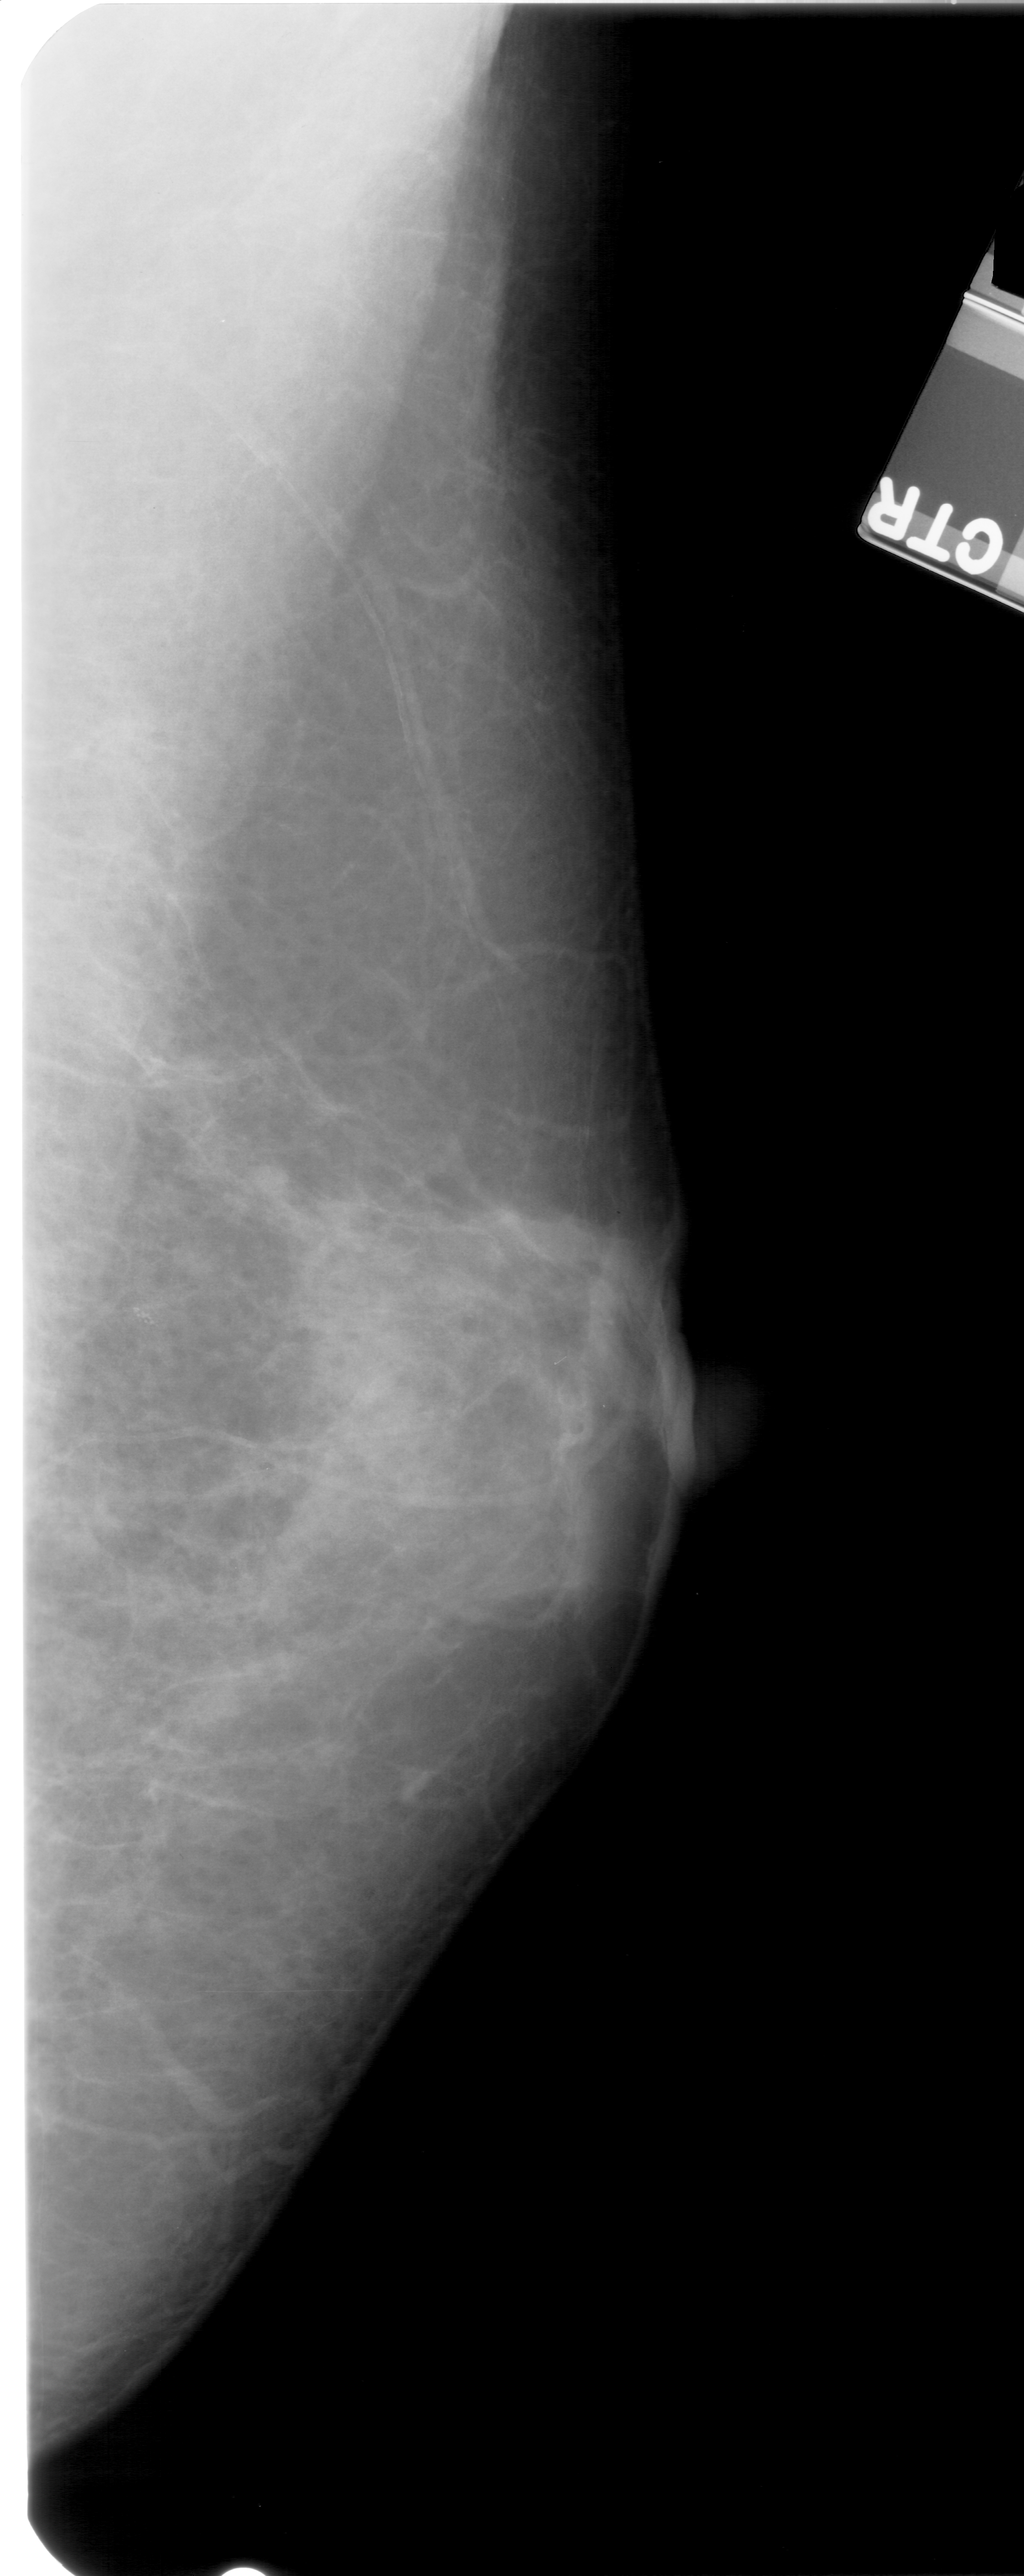
Mammogram (digitized film). Right breast. MLO view. Breast composition: extremely dense (BI-RADS density category 4 of 4). 1024 × 2576 image matrix.
Expert-marked regions of interest on this film, with their recorded descriptors:
- calcifications, morphology pleomorphic, distribution clustered; BI-RADS assessment category 4; pathology result (as recorded, not read from the image): benign: bounding box [x1, y1, x2, y2] px = [78, 1253, 205, 1380]